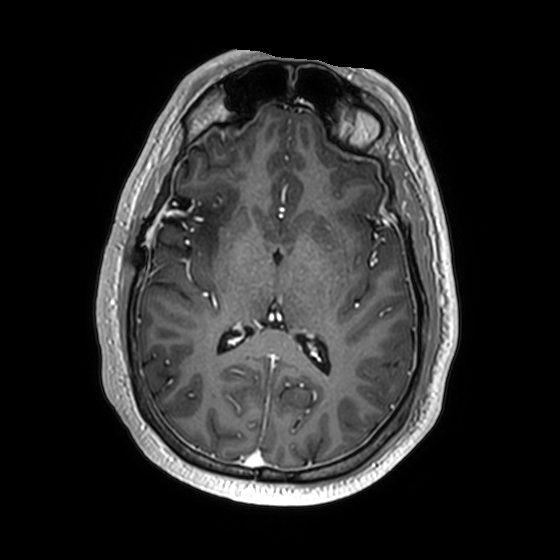
Brain MRI from a brain-tumour surgery series, one axial slice. Position 87 of 174 along the scan axis. T1-weighted post-contrast. 560 × 560 image matrix, field of view 256 × 256 mm. Case-level facts recorded for this patient, not image findings: histopathology: Astrocytoma; WHO grade: 2; IDH mutation: yes.
Outlined on this slice (expert manual segmentation):
- previous resection cavity: bounding box [x1, y1, x2, y2] px = [175, 196, 190, 211]